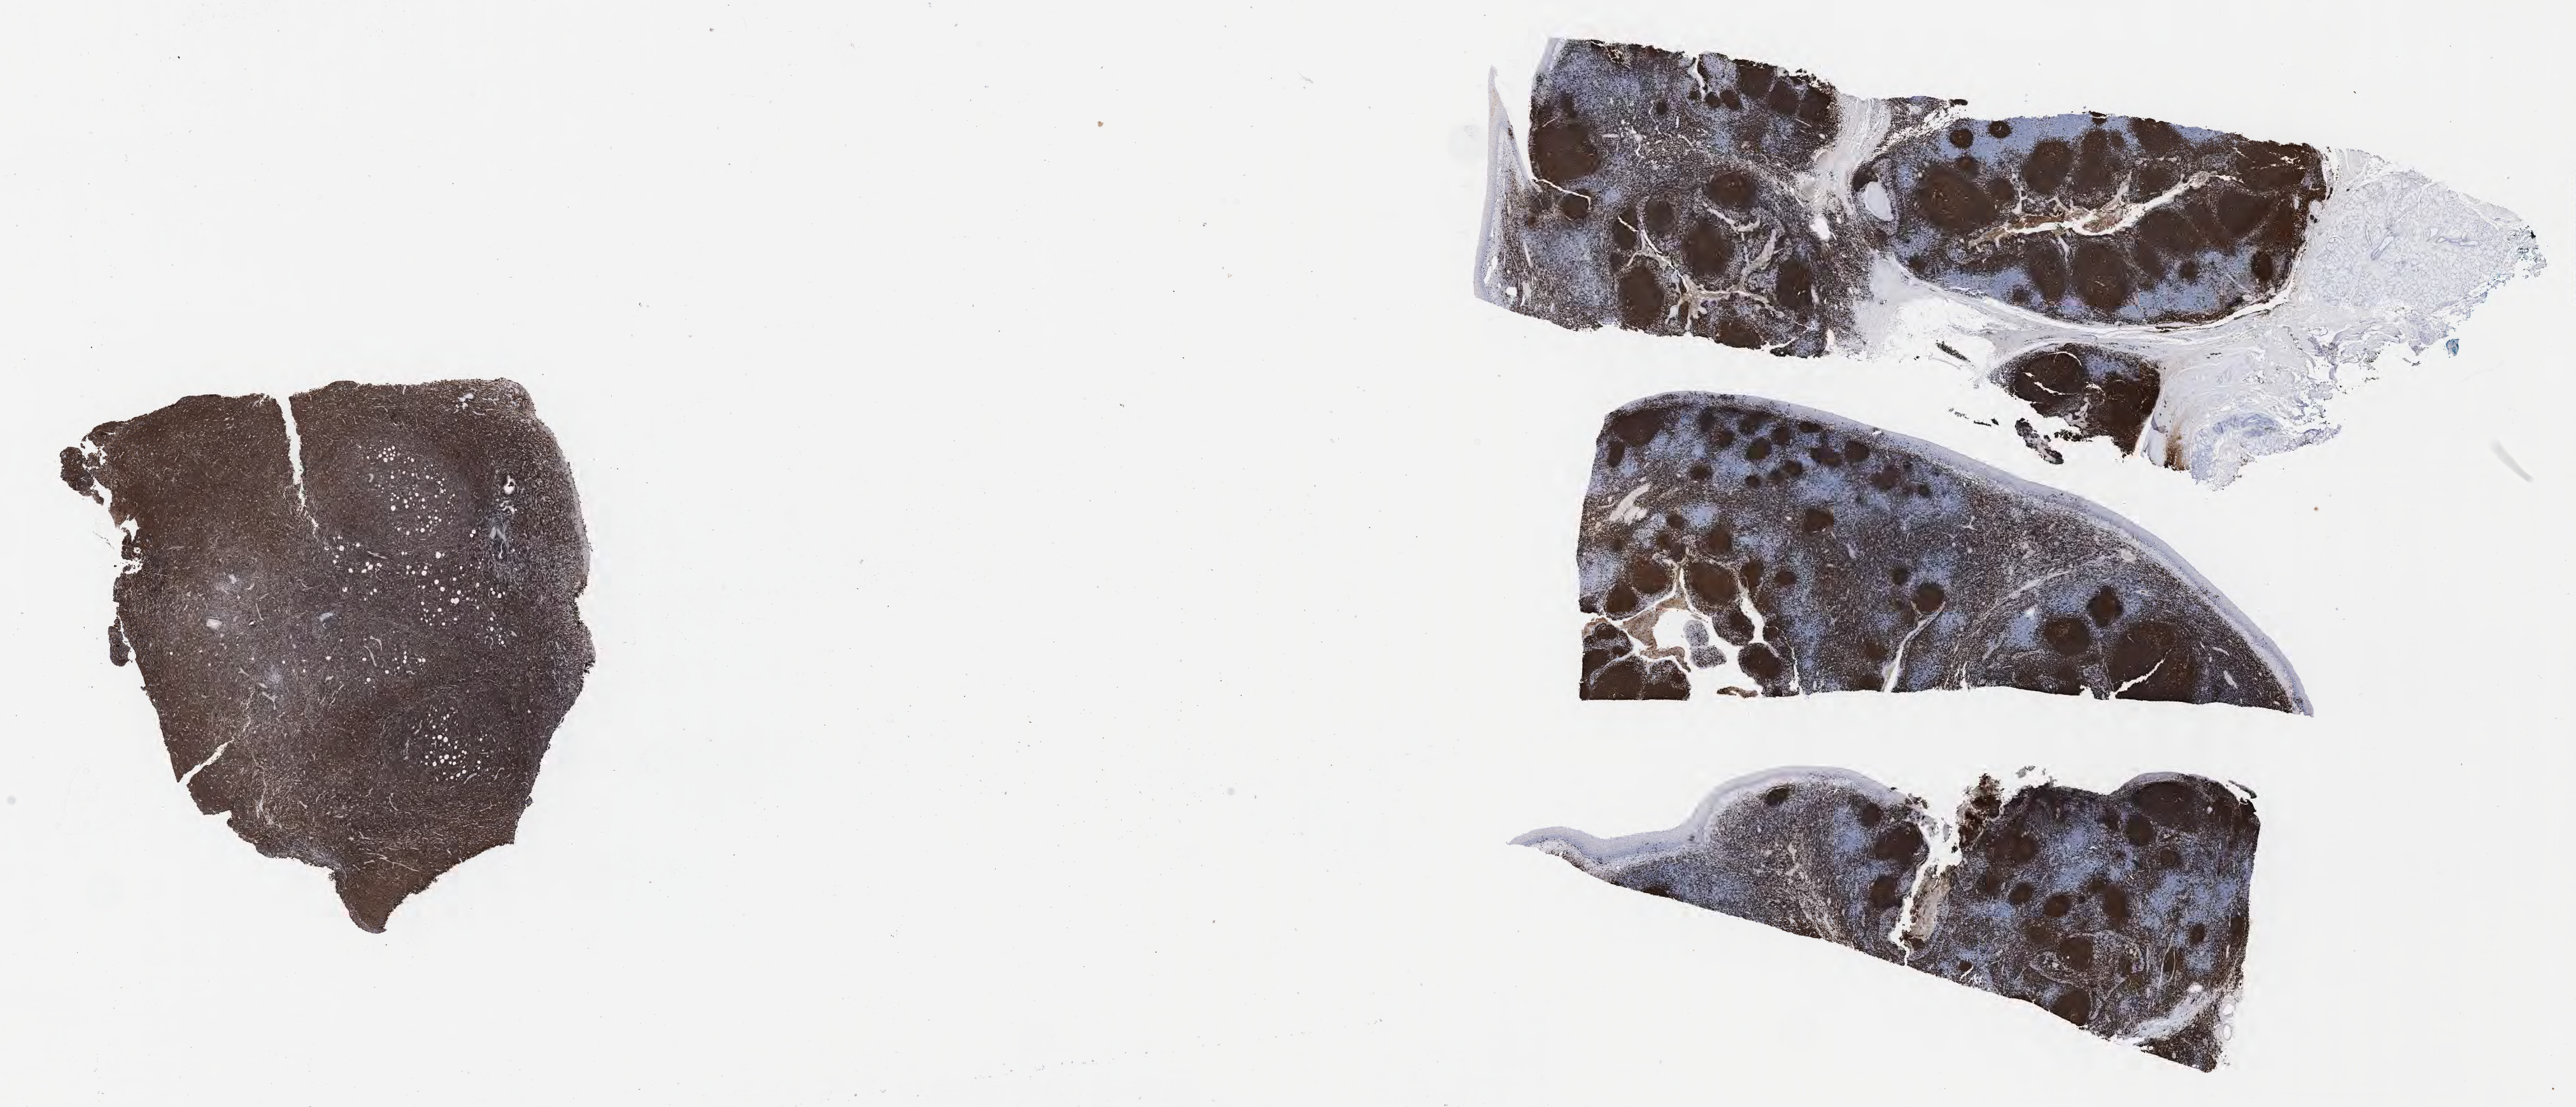
Whole-slide image, immunohistochemical stain for CD20, low-resolution overview of the scanned area, about 32.7 x 14.0 mm. Tumor tissue. Site: retroperitoneum. Male, age 7 years at initial diagnosis.
Histologic diagnosis: Diffuse large B-cell lymphoma, NOS.